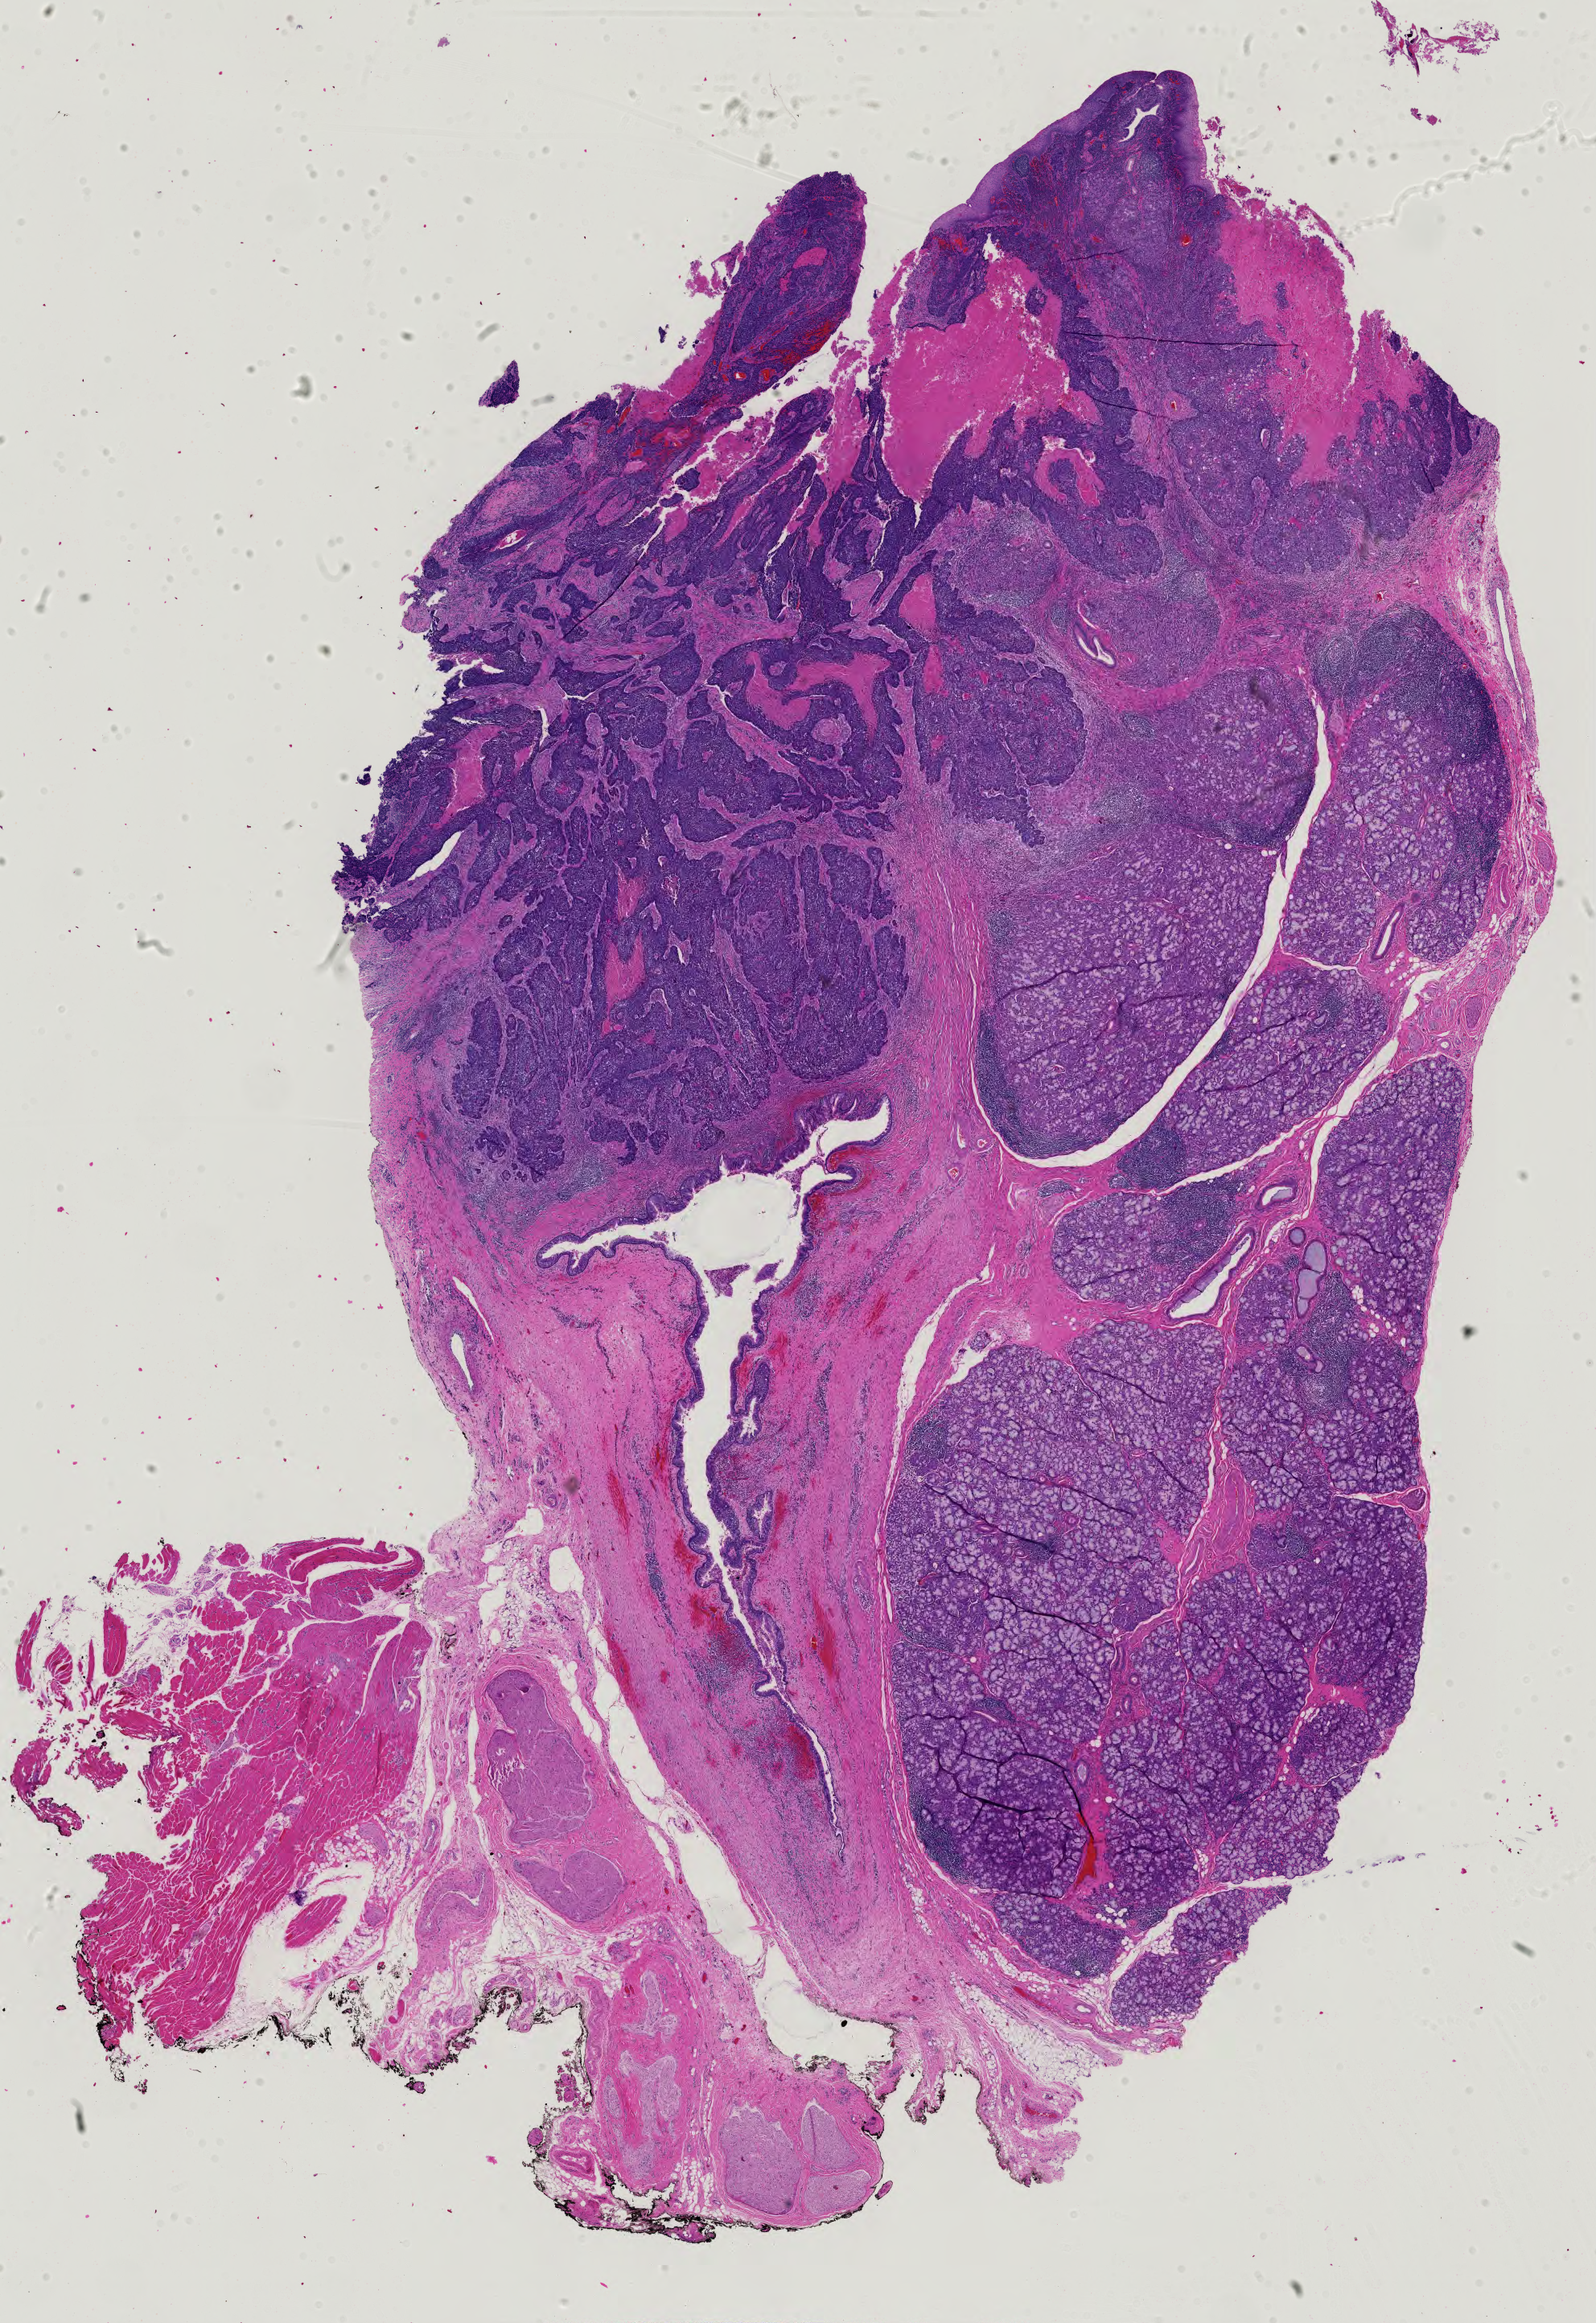
Digitized Hematoxylin and eosin (H&E) stained tissue section (whole slide), a low-resolution overview of the entire scanned area, about 14.4 x 20.9 mm. FFPE section. Primary tumour sample from the head and neck. Male patient; age at initial diagnosis 59 years.
- AJCC pathologic stage: IVA
- laterality: left
- pathologic diagnosis: Basaloid squamous cell carcinoma